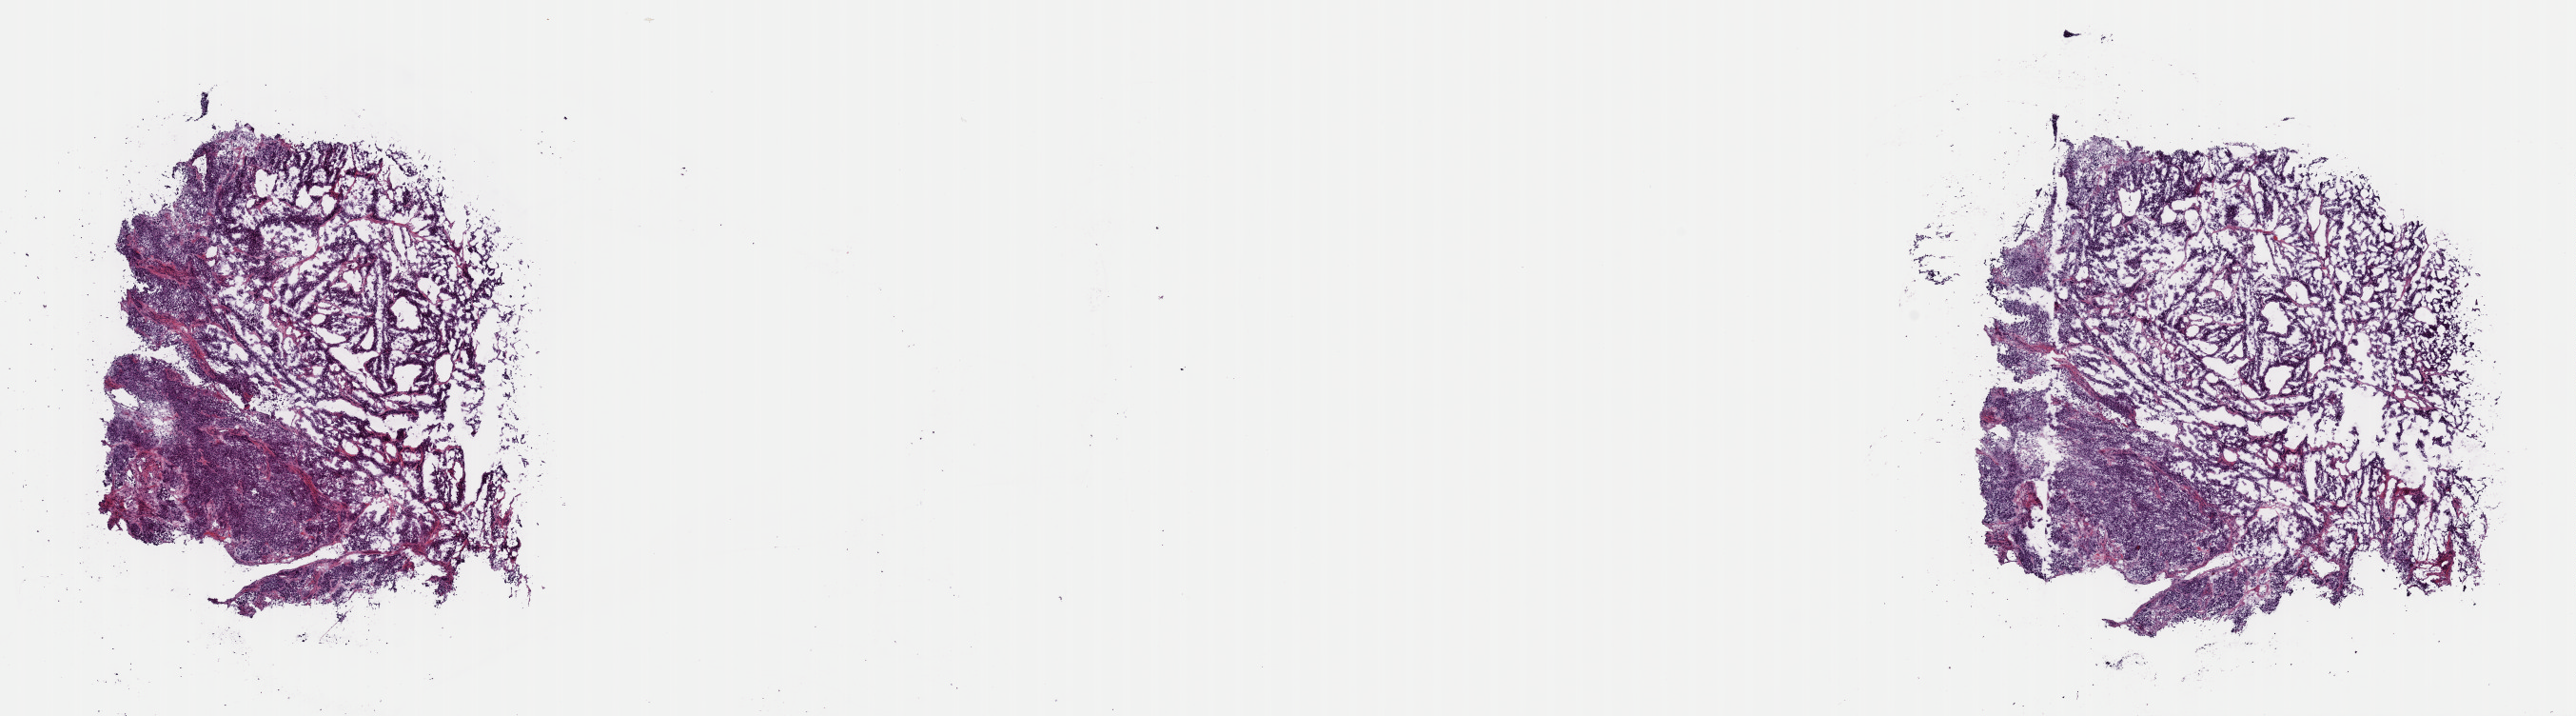
H&E-stained whole-slide image — shown as a low-resolution overview of the whole scanned area (about 21.4 x 5.9 mm); frozen section from the top of the tissue portion; sample: primary tumour, adrenal cortex. Patient: female, age at initial diagnosis 42 years. Slide review estimates, as recorded: tumour cells 95%, tumour nuclei 98%, normal cells 0%, stromal cells 5%, necrosis 0%. Inflammatory infiltration, as recorded: lymphocyte infiltration 0%, monocyte infiltration 0%, neutrophil infiltration 0%.
• diagnosis: Adrenal cortical carcinoma (cortex of adrenal gland)